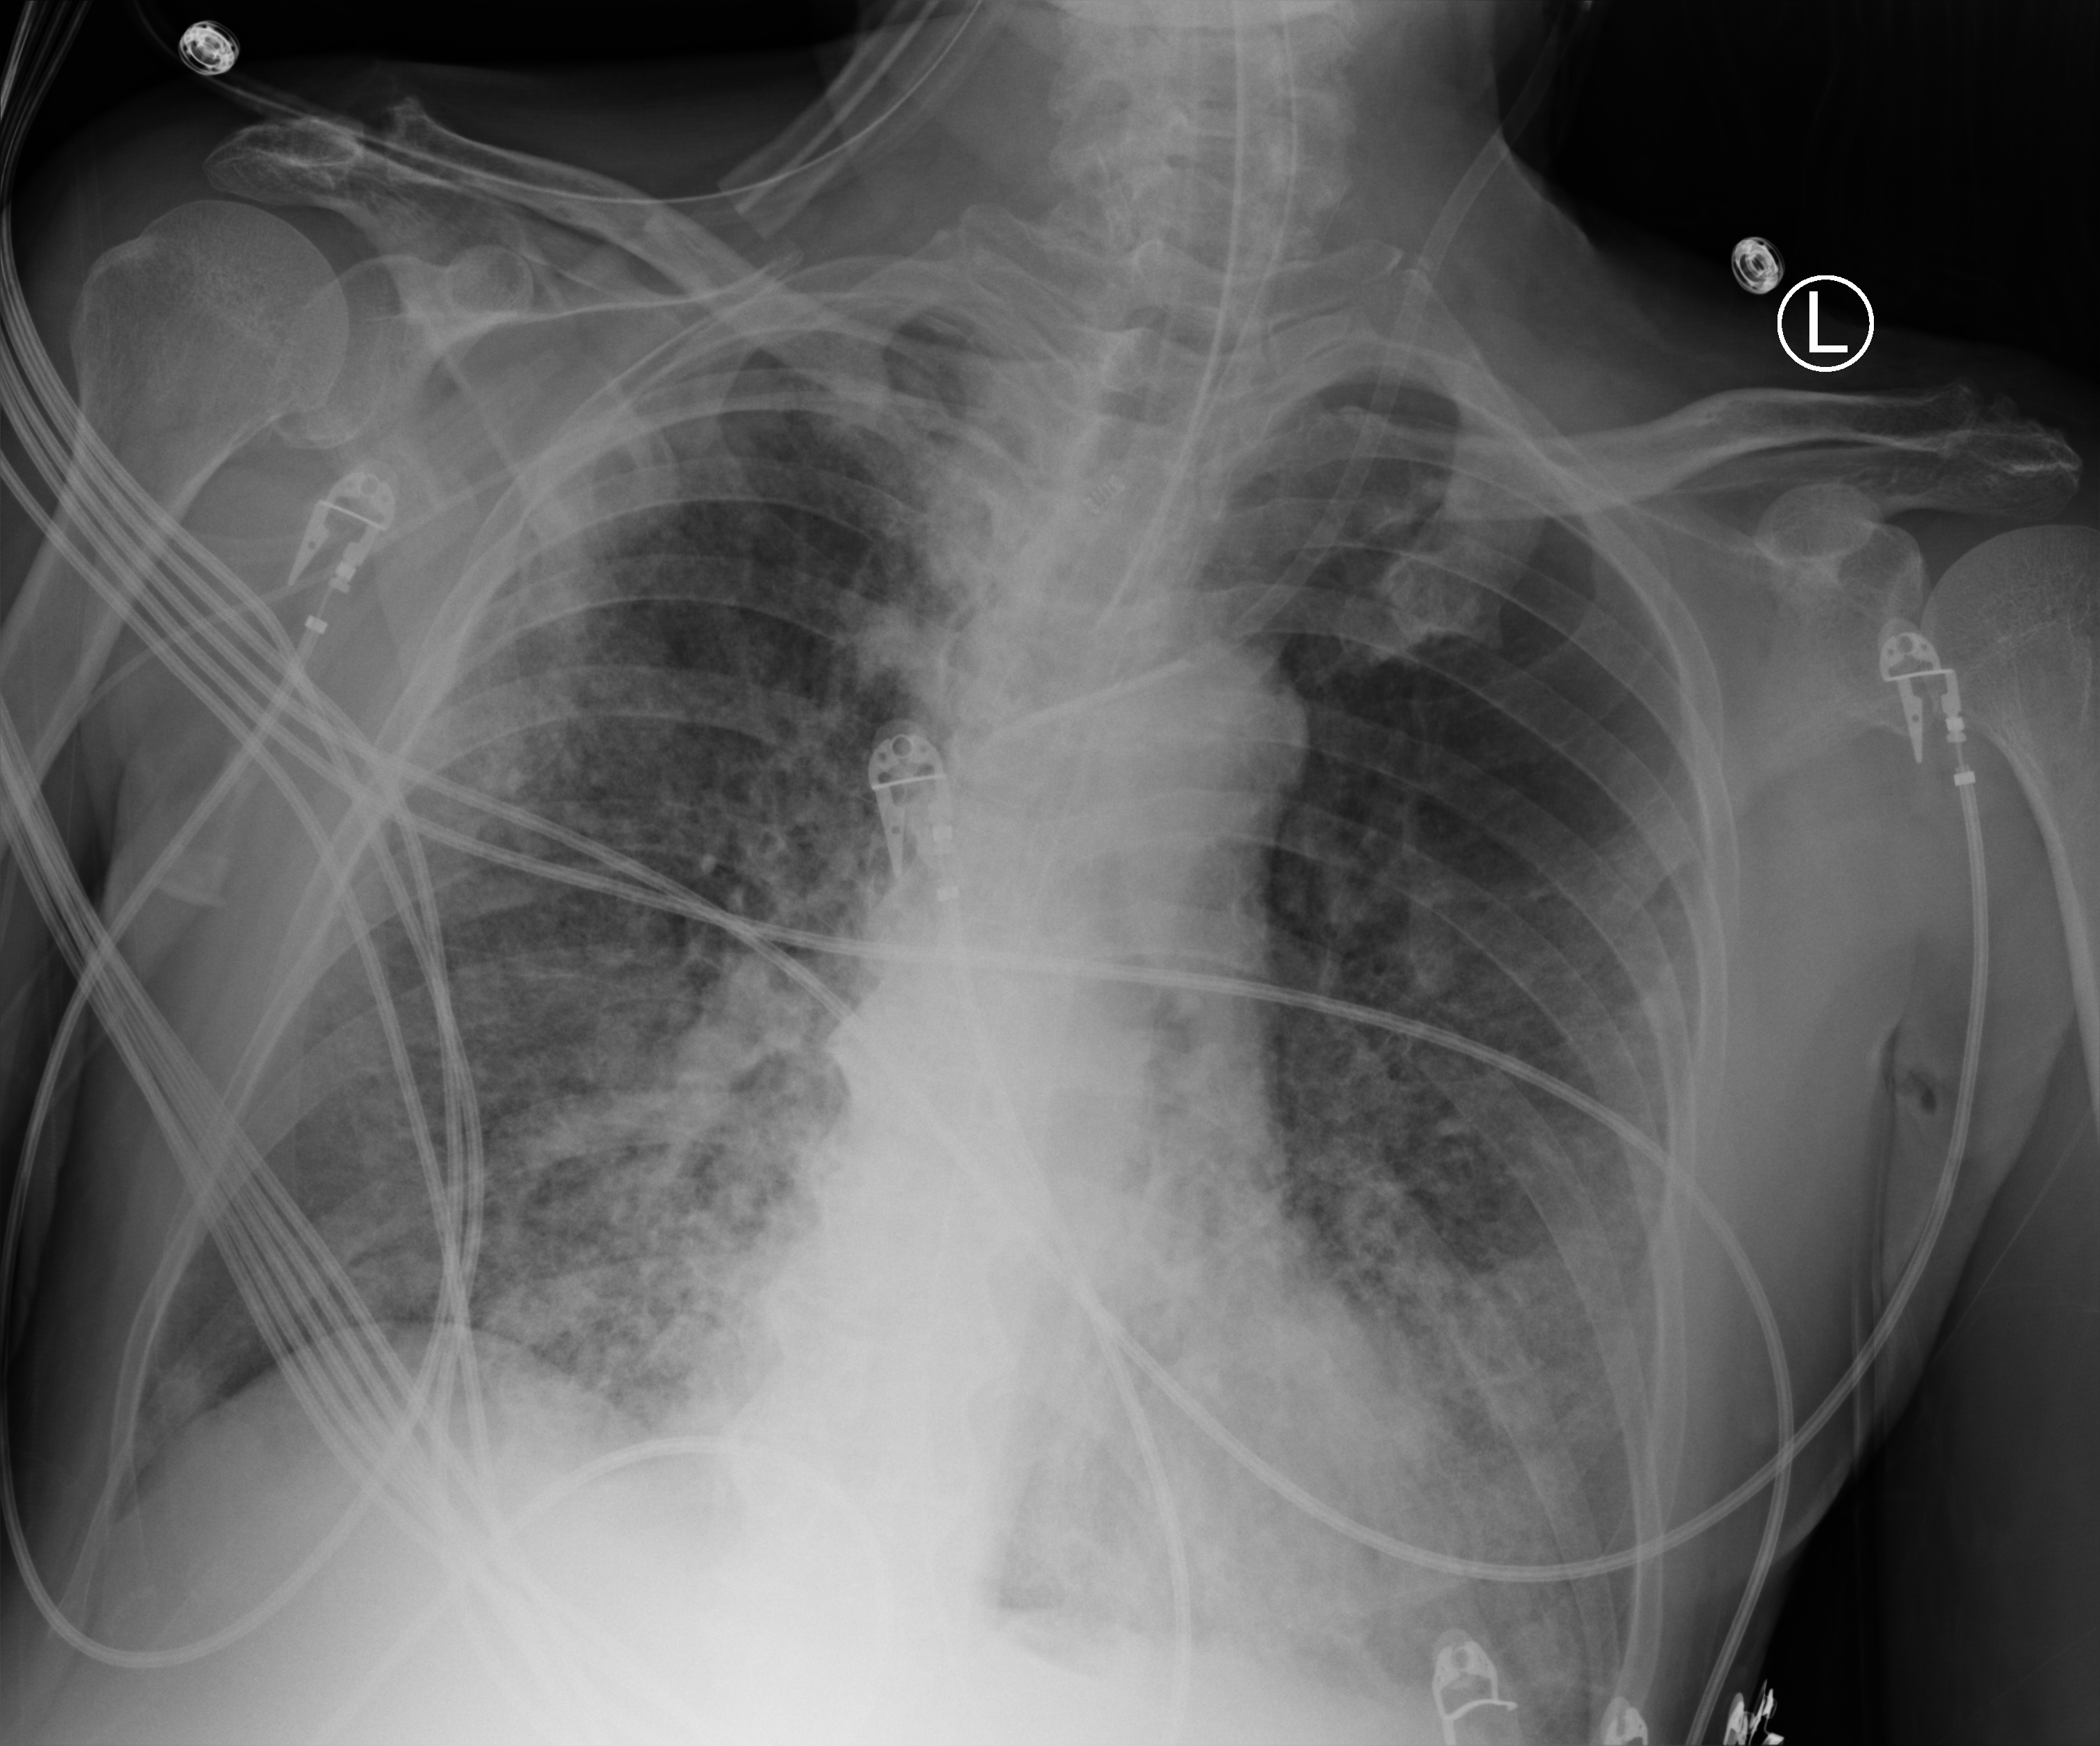
Chest X-ray (portable), anteroposterior (AP) projection. Patient hospitalised with COVID-19; male, aged 60–74 years.
From the hospital-stay record, not from the radiograph (when in the stay this image was taken is not recorded): hypertension (admission record): yes; mechanically ventilated during this hospital stay: yes.